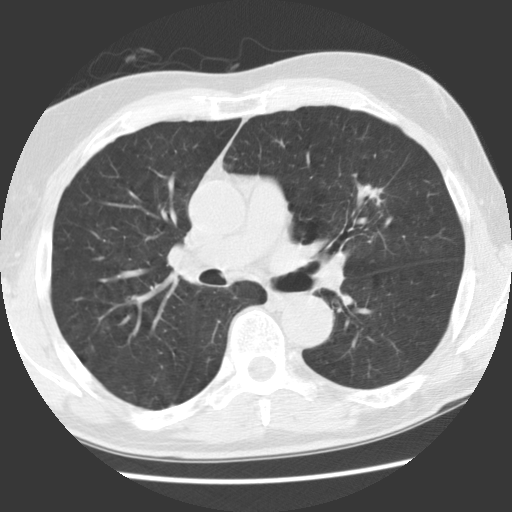
Low-dose screening chest CT, axial slice, baseline screening round, lung window (W 1500 / L -600 HU), 512 × 512 image matrix, field of view 320 × 320 mm. Male, age 70 years at enrolment.
Lesion marked by an expert reader, bounding box <340,171,398,221> (left, top, right, bottom; pixels). The screening reader recorded 2 non-calcified nodules or masses ≥4 mm on this exam (left upper lobe, right lower lobe); which of them this box marks is not recorded. Official screen result: positive, change unspecified: nodule(s) >= 4 mm or enlarging nodule(s), mass(es), or other non-specific abnormalities suspicious for lung cancer. Participant outcome: lung cancer diagnosed 879 days after this screen — adenocarcinoma, NOS, left upper lobe, moderately differentiated (G2), stage IIIA (AJCC 6th edition), 17 mm at pathology.